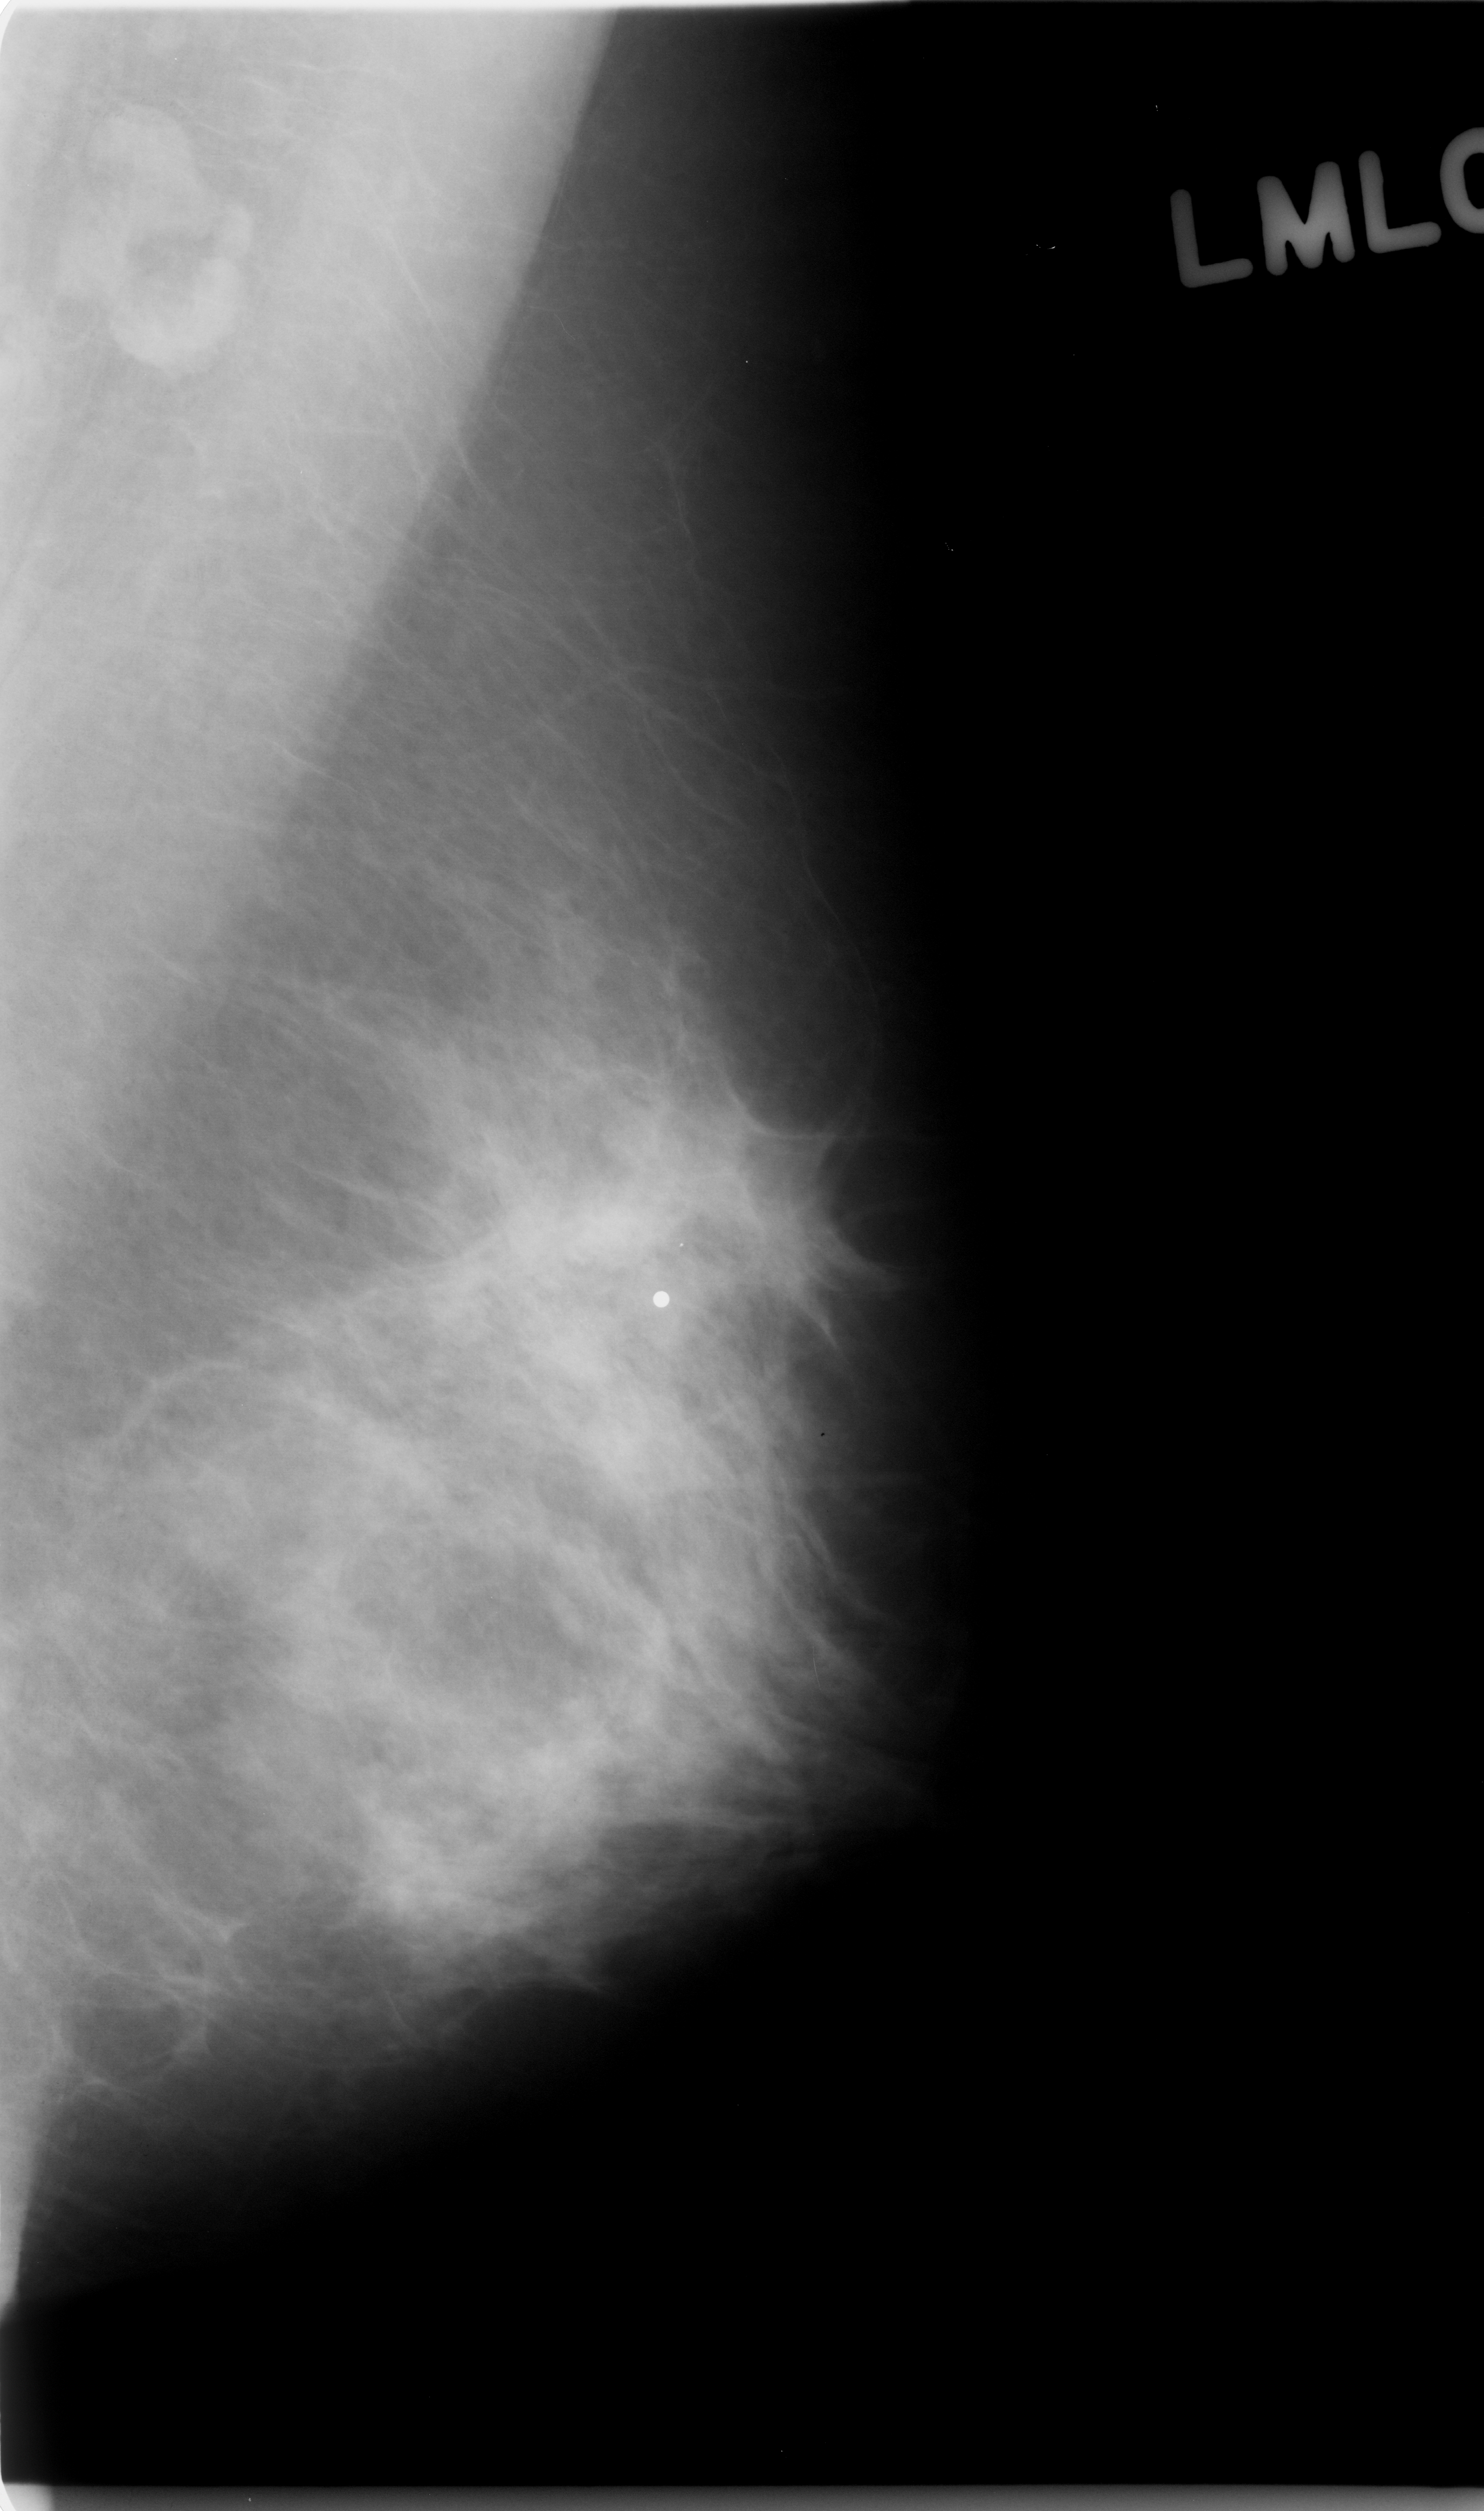
Scanned film-screen mammogram; left breast; mediolateral oblique (MLO) view; BI-RADS breast density category 2 (scale 1–4); 1484 × 2511 image matrix.
Expert-marked regions of interest on this film, with their recorded descriptors:
- calcifications, morphology amorphous, distribution clustered; BI-RADS assessment category 4; pathology result (as recorded, not read from the image): malignant: bounding box (x1, y1, x2, y2) in pixels: (521, 966, 1023, 1416)